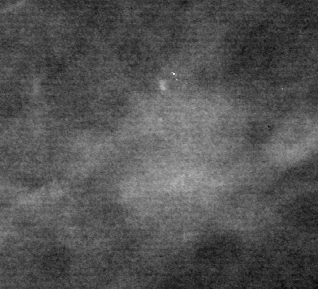
Cropped region of a digitized screen-film mammogram centred on a radiologist-marked abnormality; left breast; CC view.
Marked abnormality: mass, shape lobulated, margins microlobulated; BI-RADS assessment category 5; subtlety rating 4 on a 1 (subtle) to 5 (obvious) scale; pathology result (as recorded, not read from the image): malignant.